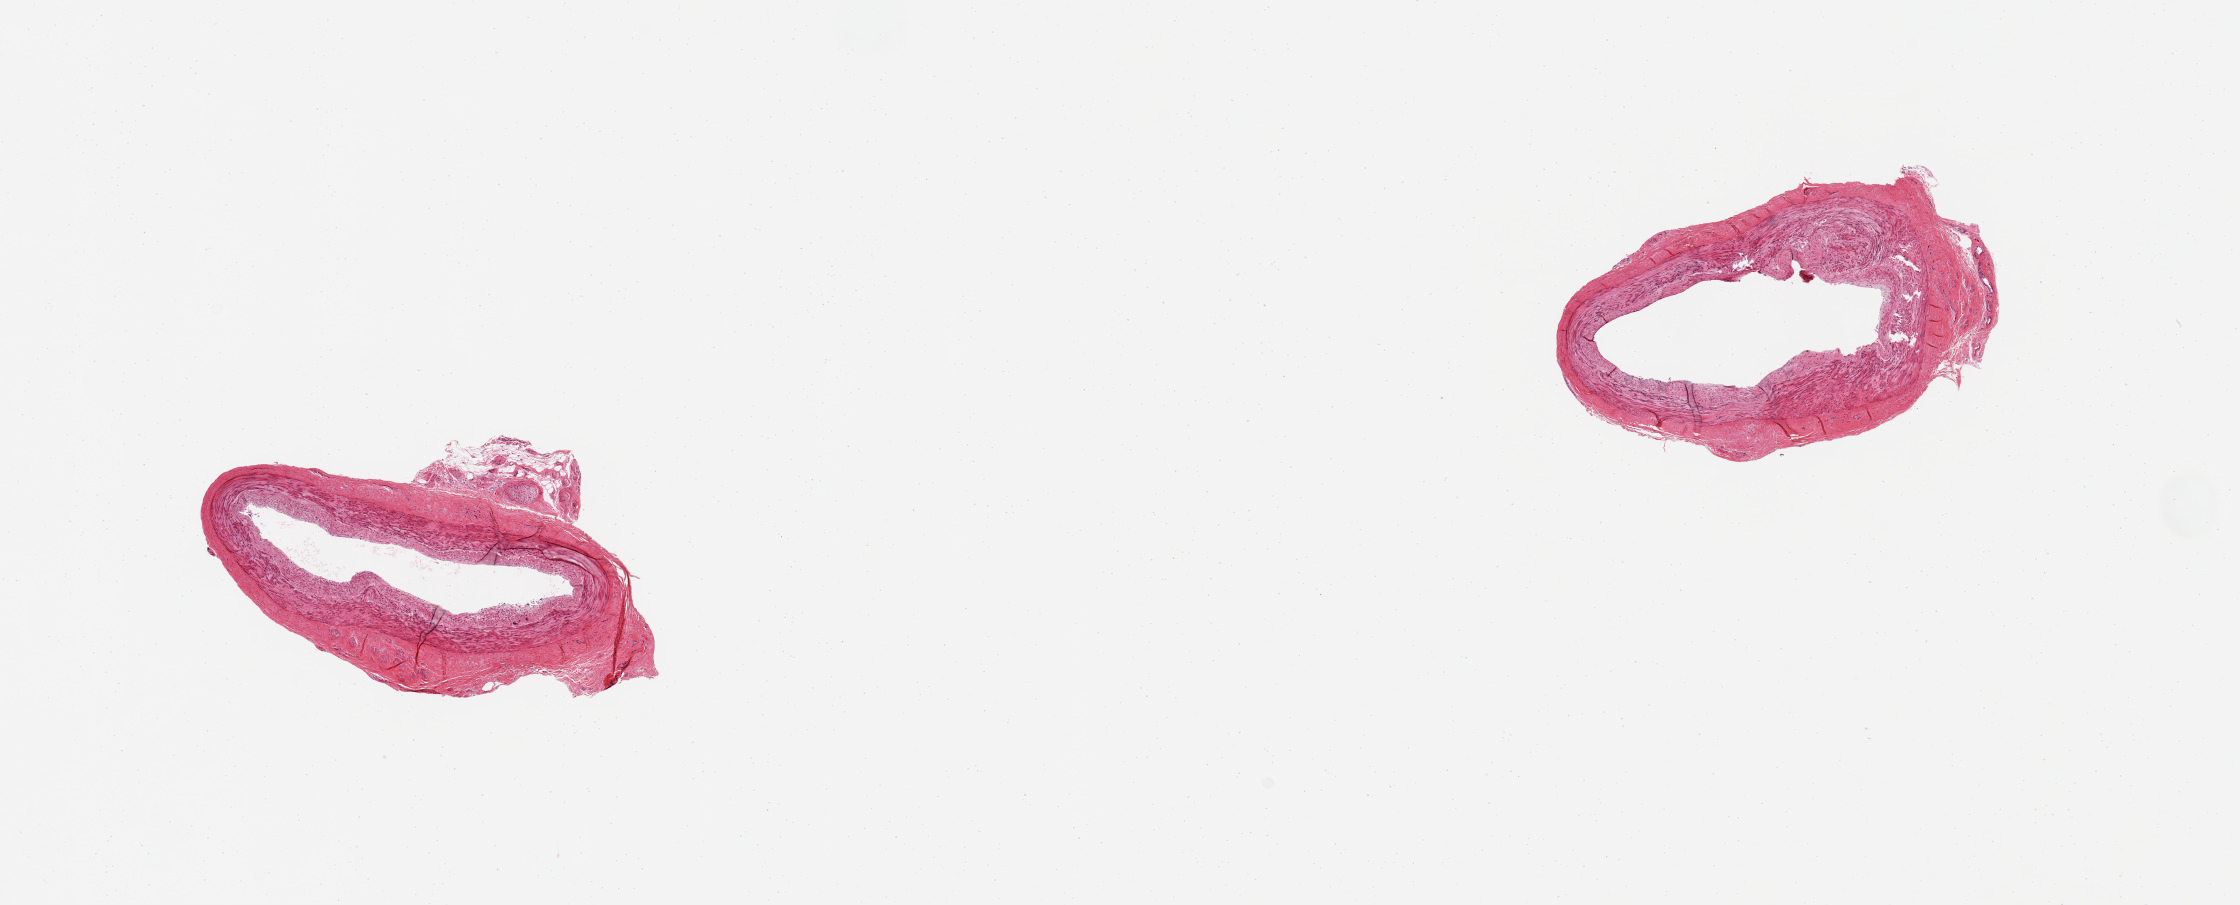
Whole-slide image, haematoxylin and eosin stain, whole scanned area (about 17.7 x 7.2 mm, from a 20x scan) shown as a low-resolution overview, PAXgene-fixed paraffin-embedded (PFPE) section, sampled site (target tissue): tibial artery, donor tissue sample. Donor: male.
- pathologist's review note for this sample: 2 pieces; relatively well trimmed, small attachment of fat and nerve on one piece